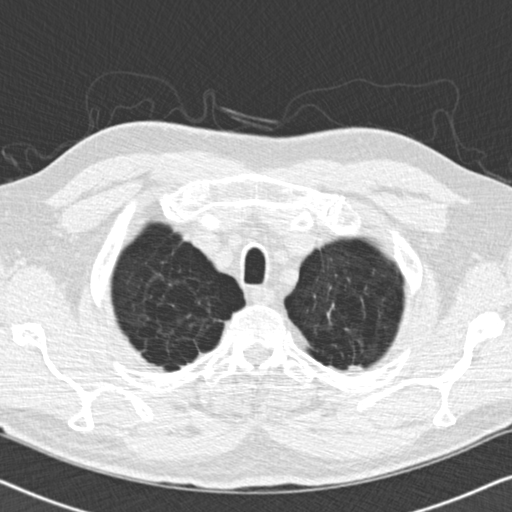
Low-dose screening chest CT, one axial slice. Position 158 of 175 along the scan axis. 120 kVp. Lung window (W 1500 / L -600 HU). 2 mm slice thickness. 512 × 512 image matrix.
Annotated regions visible in this slice (expert manual segmentation):
- lesion 1 (tumor, upper lobe of left lung): bounding box [x1, y1, x2, y2] px = [348, 365, 364, 371]